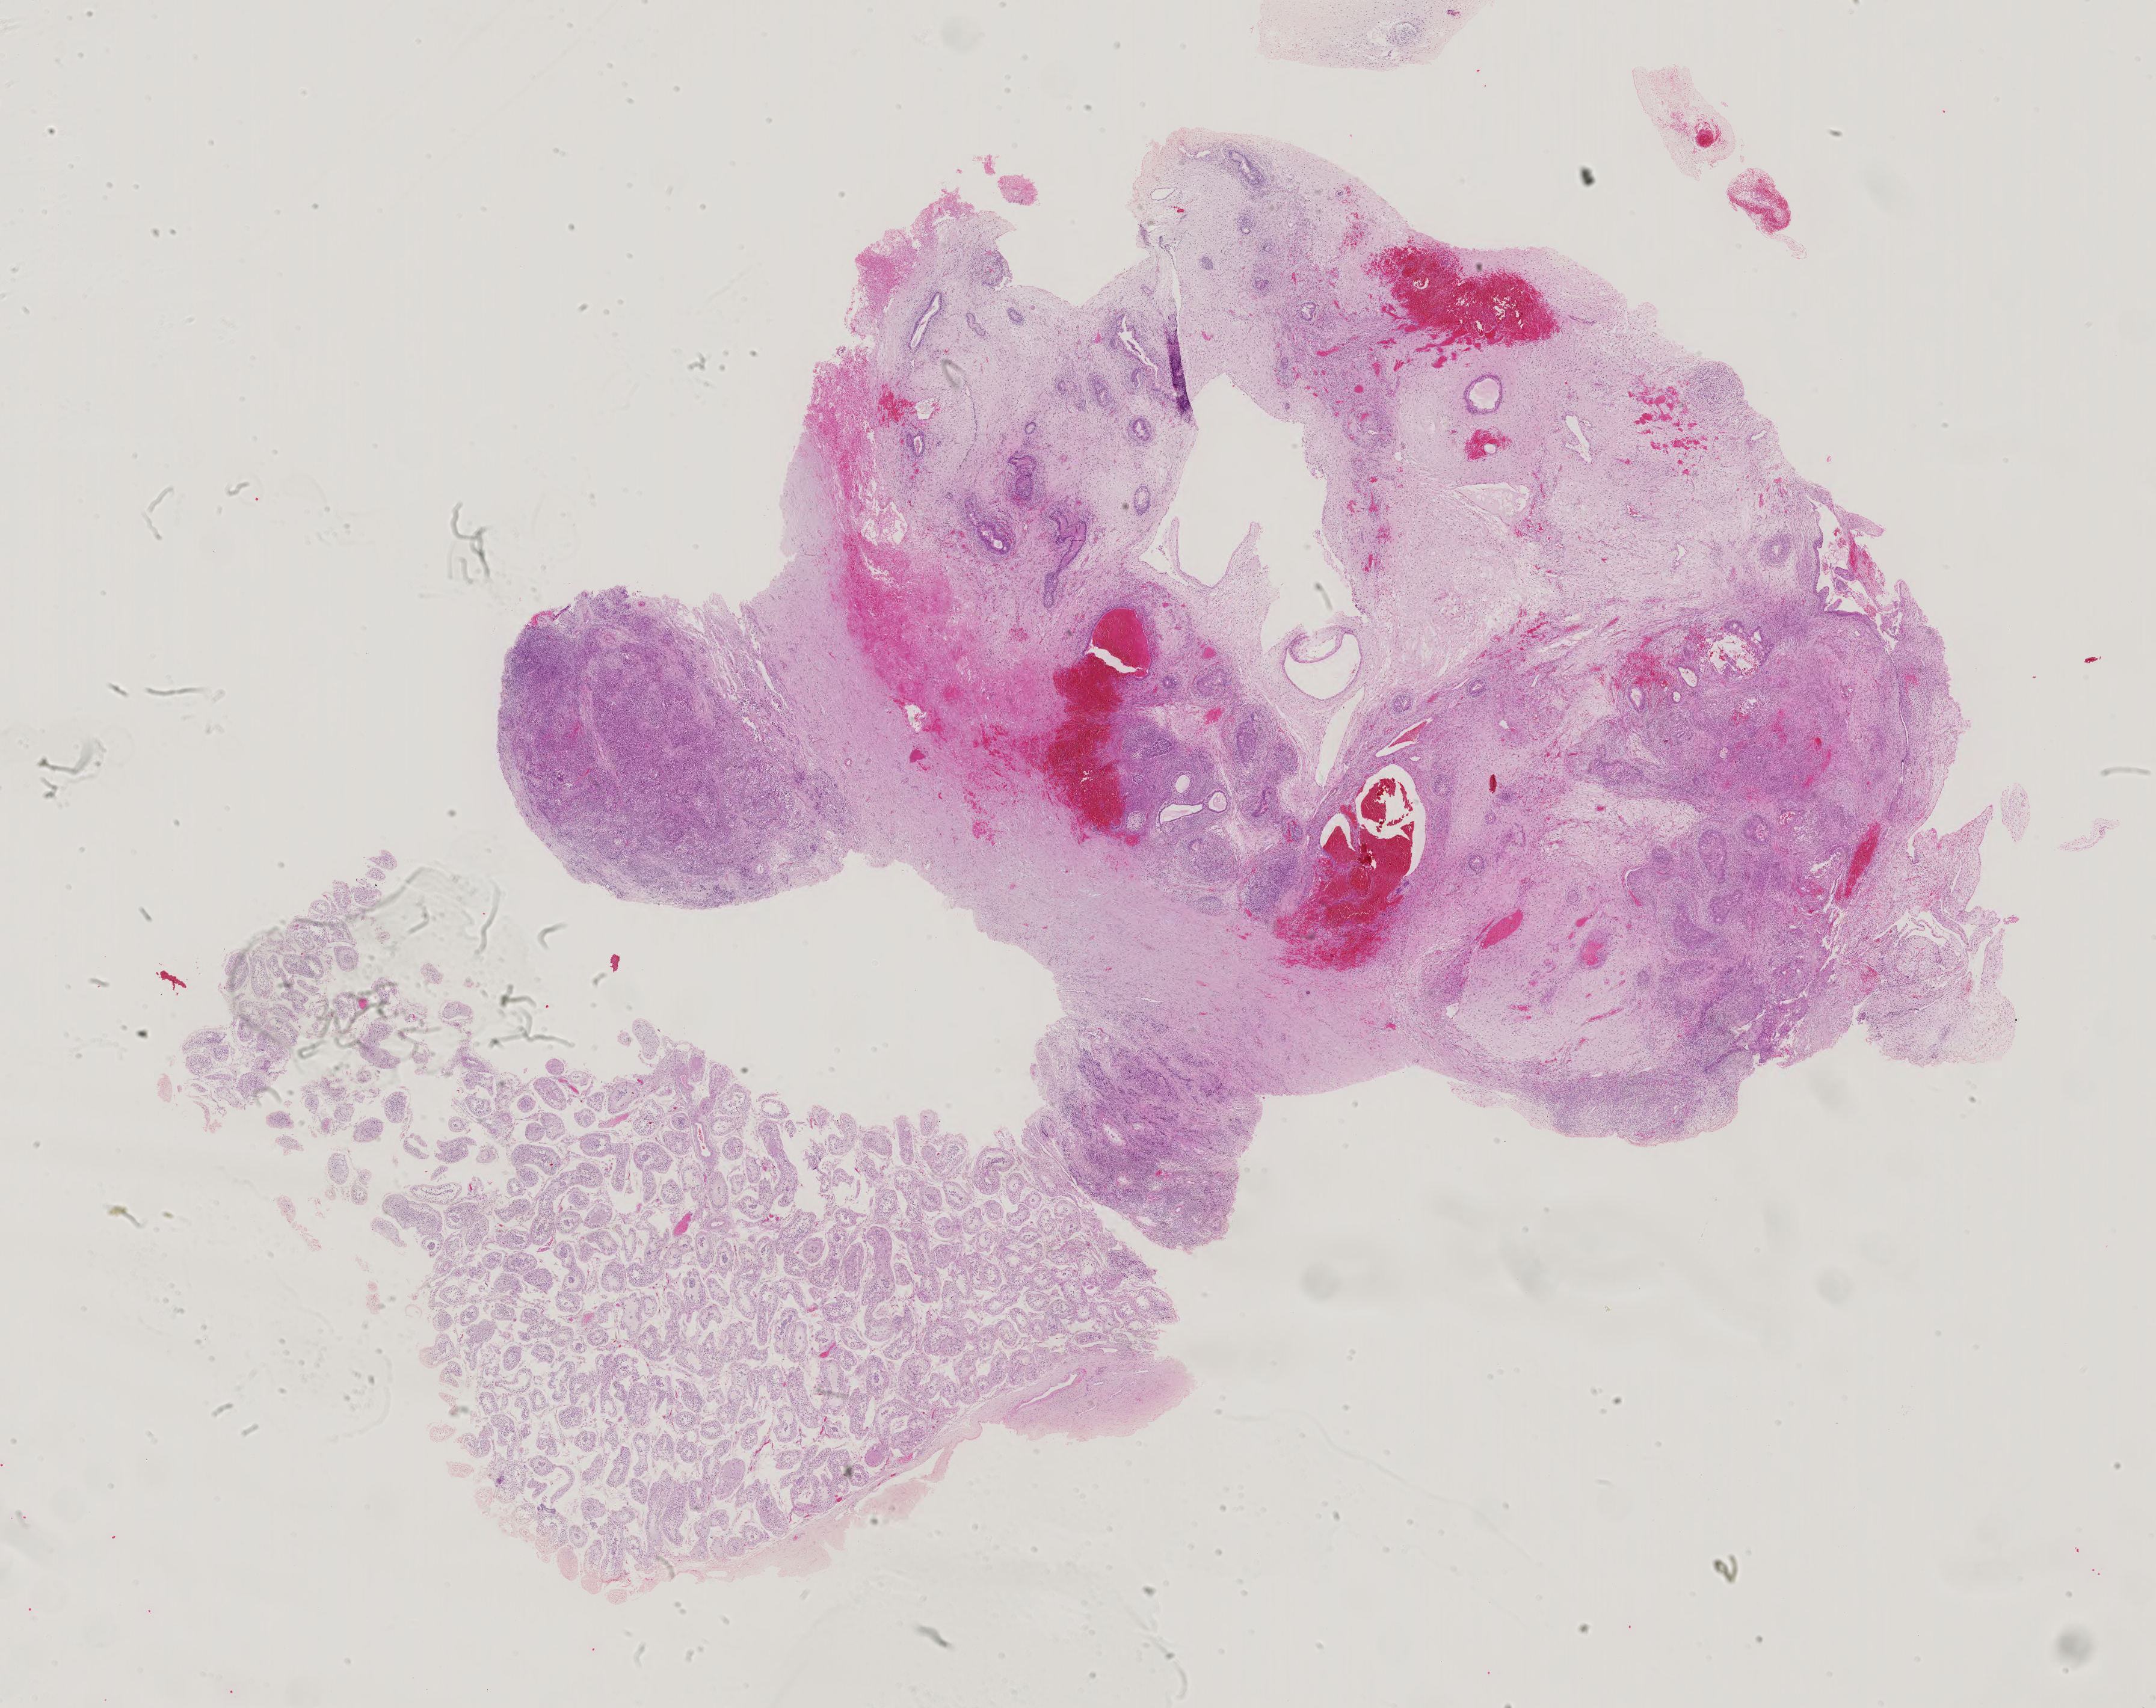
Whole-slide histology image, Hematoxylin and eosin (H&E) stained — low-resolution overview of the scanned area, about 26.1 x 20.7 mm (slide scanned at 40x). Patient sex: male.
* specimen: FFPE section; primary tumour sample from the testis